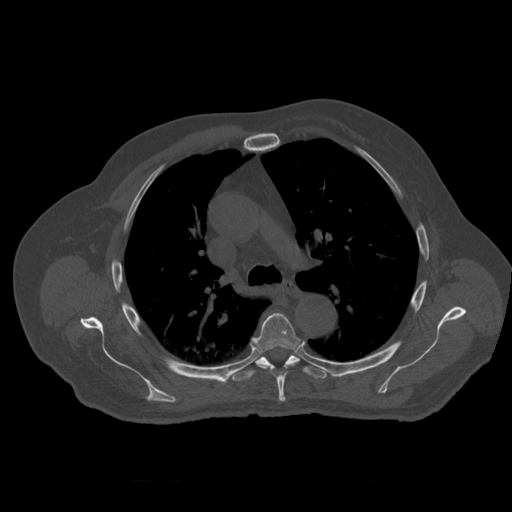
CT including the spine, one axial slice. Slice 393 of 399 in the series (ordered by position). Reconstruction kernel STANDARD. Bone window (W 1800 / L 400 HU). 1.25 mm slice thickness. 512 × 512 image matrix, field of view 407 × 407 mm. Patient age 73 years. From the clinical record (not read from this slice): primary cancer: prostate; vertebrae with lytic lesions (as recorded): L2.
Outlined on this slice (semi-automatically segmented with operator editing):
- T5 vertebra: box from (x=252, y=313) to (x=304, y=402) px
- T6 vertebra: (x=232, y=355)–(x=327, y=382)